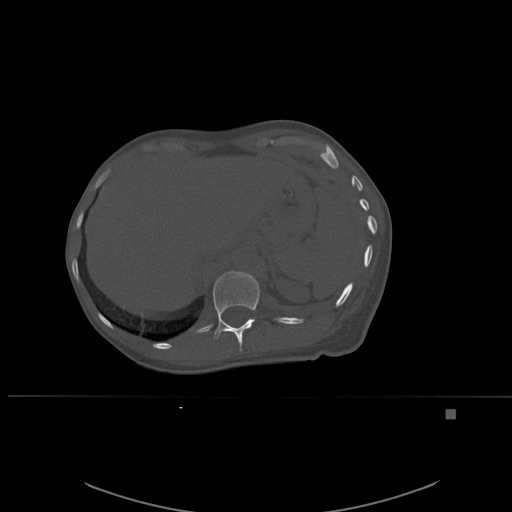
CT including the spine, one axial slice. Slice 279 of 537 in the series (ordered by position). Bone window (W 1800 / L 400 HU). 1.5 mm slice thickness. 512 × 512 image matrix, field of view 440 × 440 mm. Patient: female, 45 years. Case-level facts recorded for this patient, not image findings: primary cancer: lung.
Annotated regions visible in this slice (semi-automatic segmentation, software-assisted and operator-edited):
- T12 vertebra: bounding box [x1, y1, x2, y2] px = [213, 270, 260, 352]